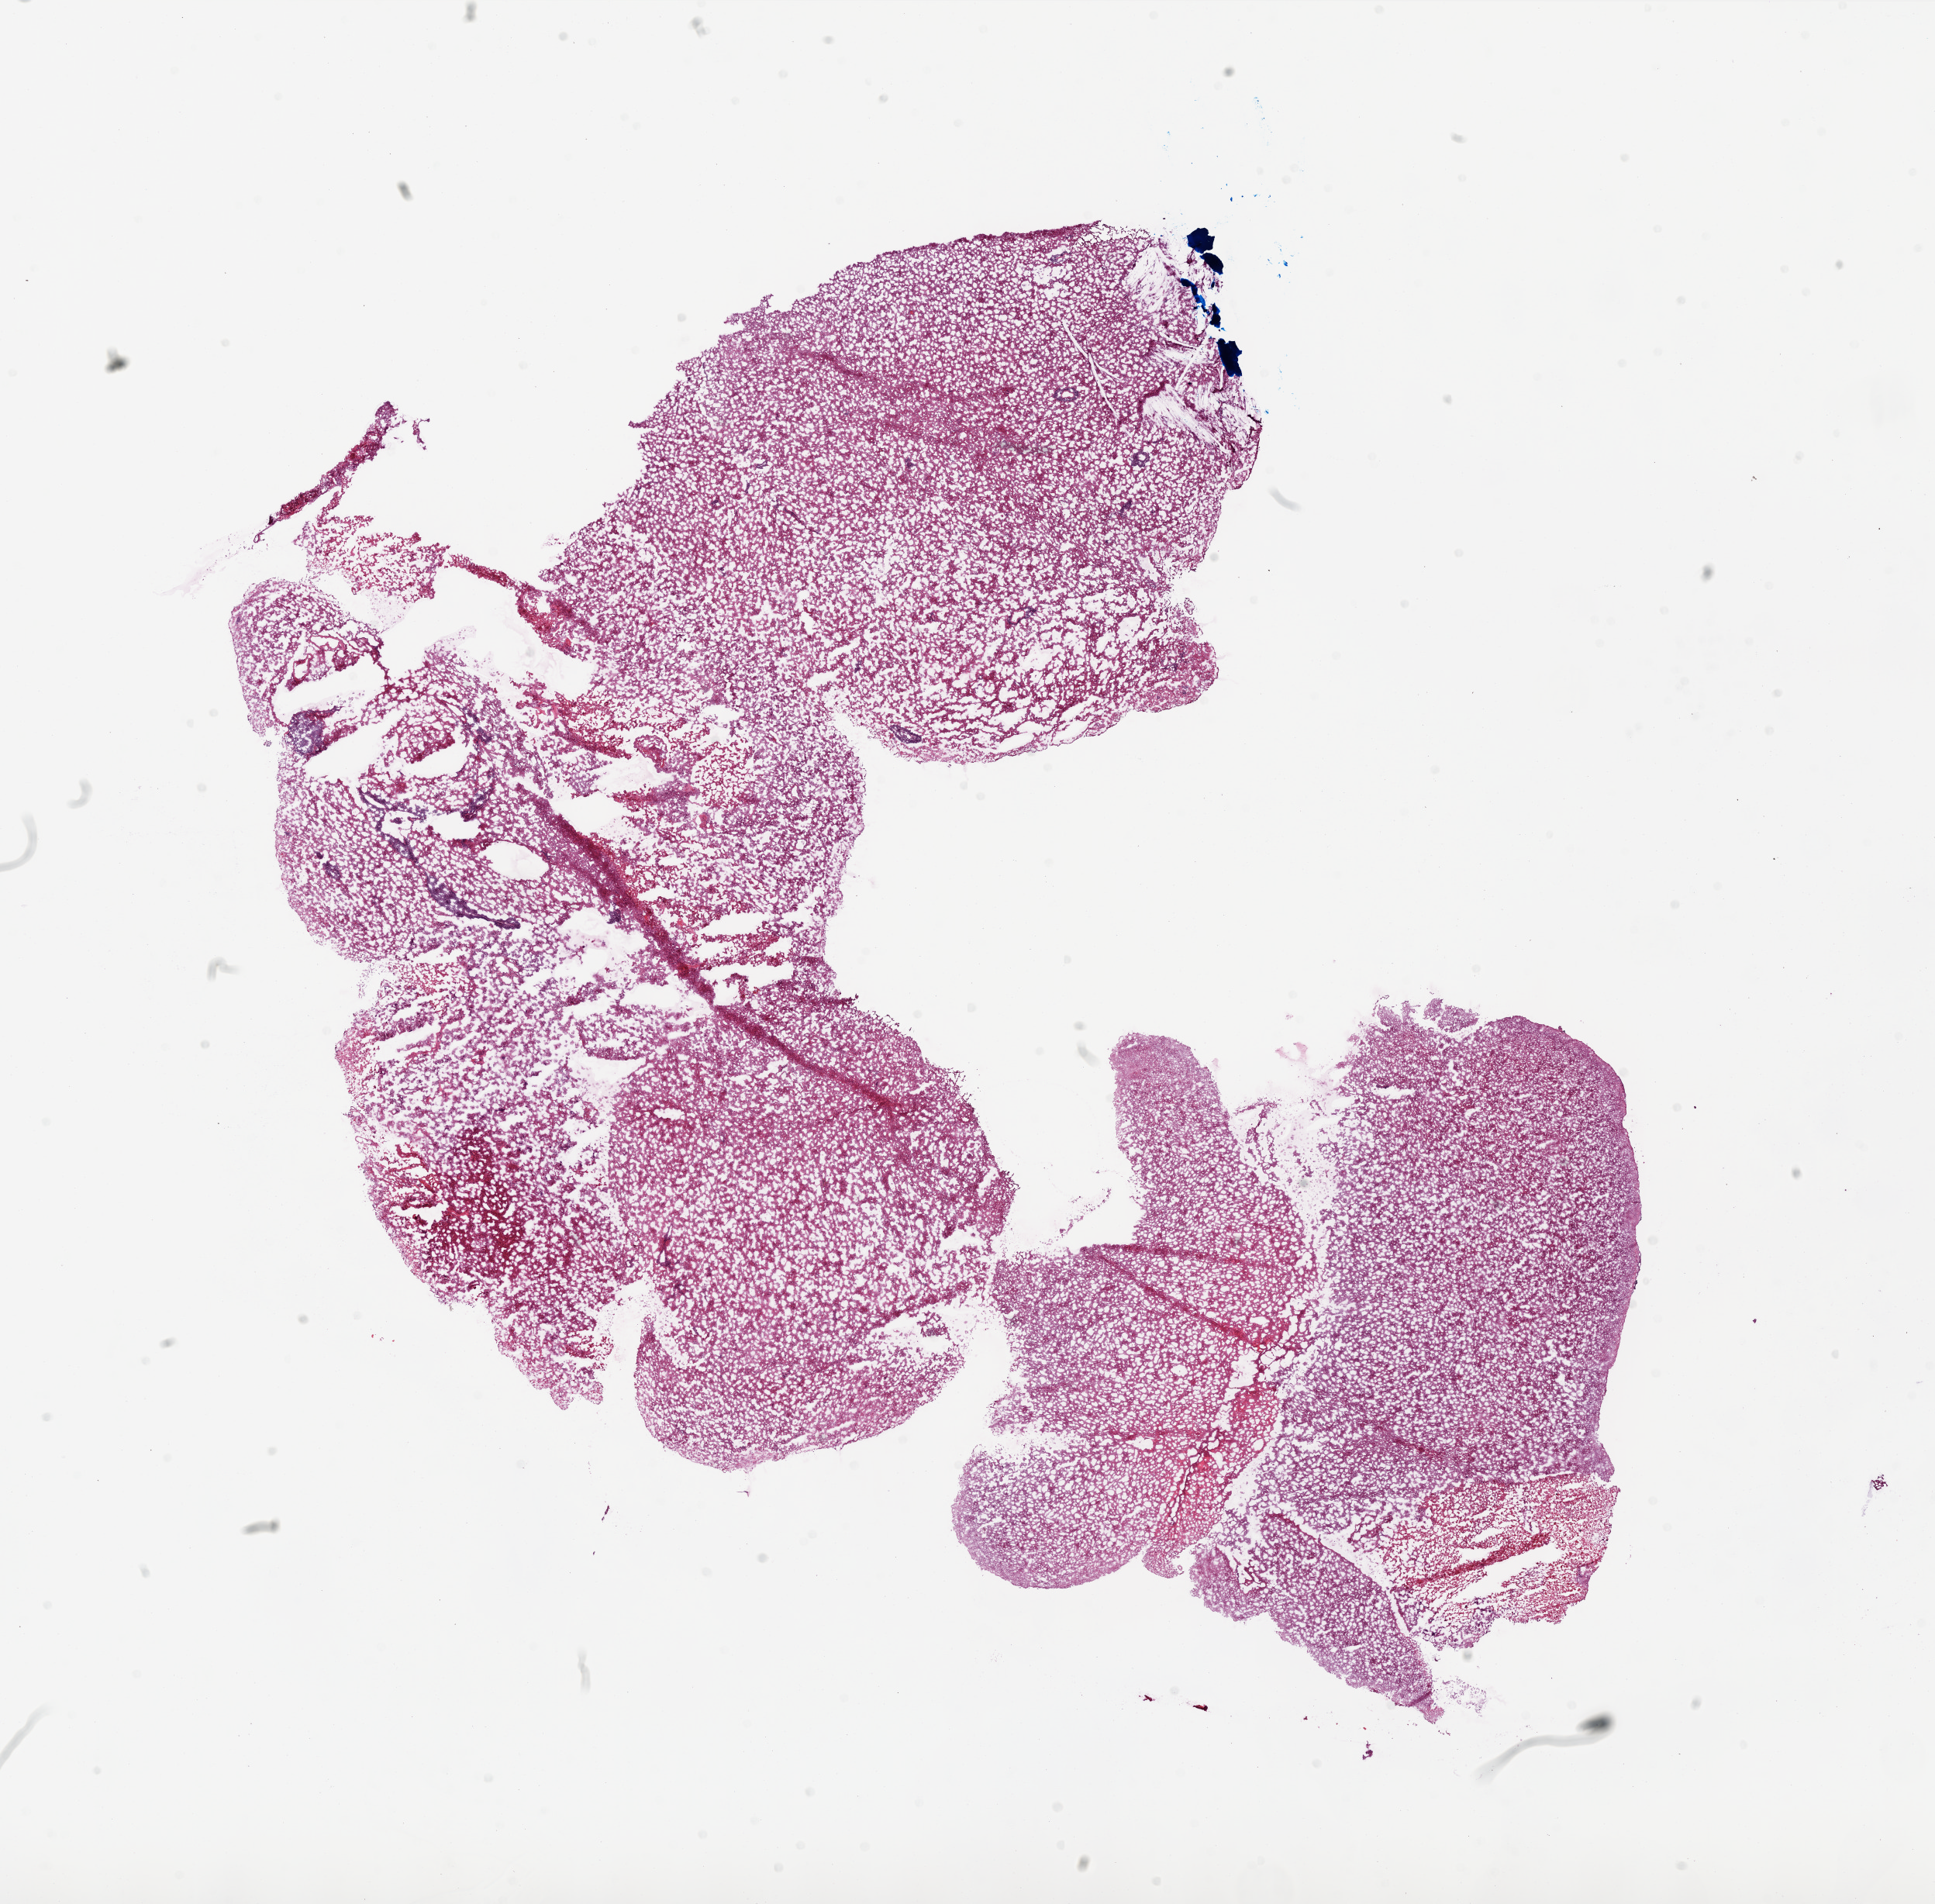
Whole-slide histology image, H&E — shown as a low-resolution overview of the whole scanned area (about 20.0 x 19.7 mm); frozen section; sample: primary tumour, brain. Female patient; age at initial diagnosis 51 years. Slide review estimates, as recorded: tumour cells 100%, tumour nuclei 97%, normal cells 0%, stromal cells 0%, necrosis 0%. Inflammatory infiltration, as recorded: lymphocyte infiltration 100%, monocyte infiltration 0%, neutrophil infiltration 0%.
Diagnosis: Glioblastoma.